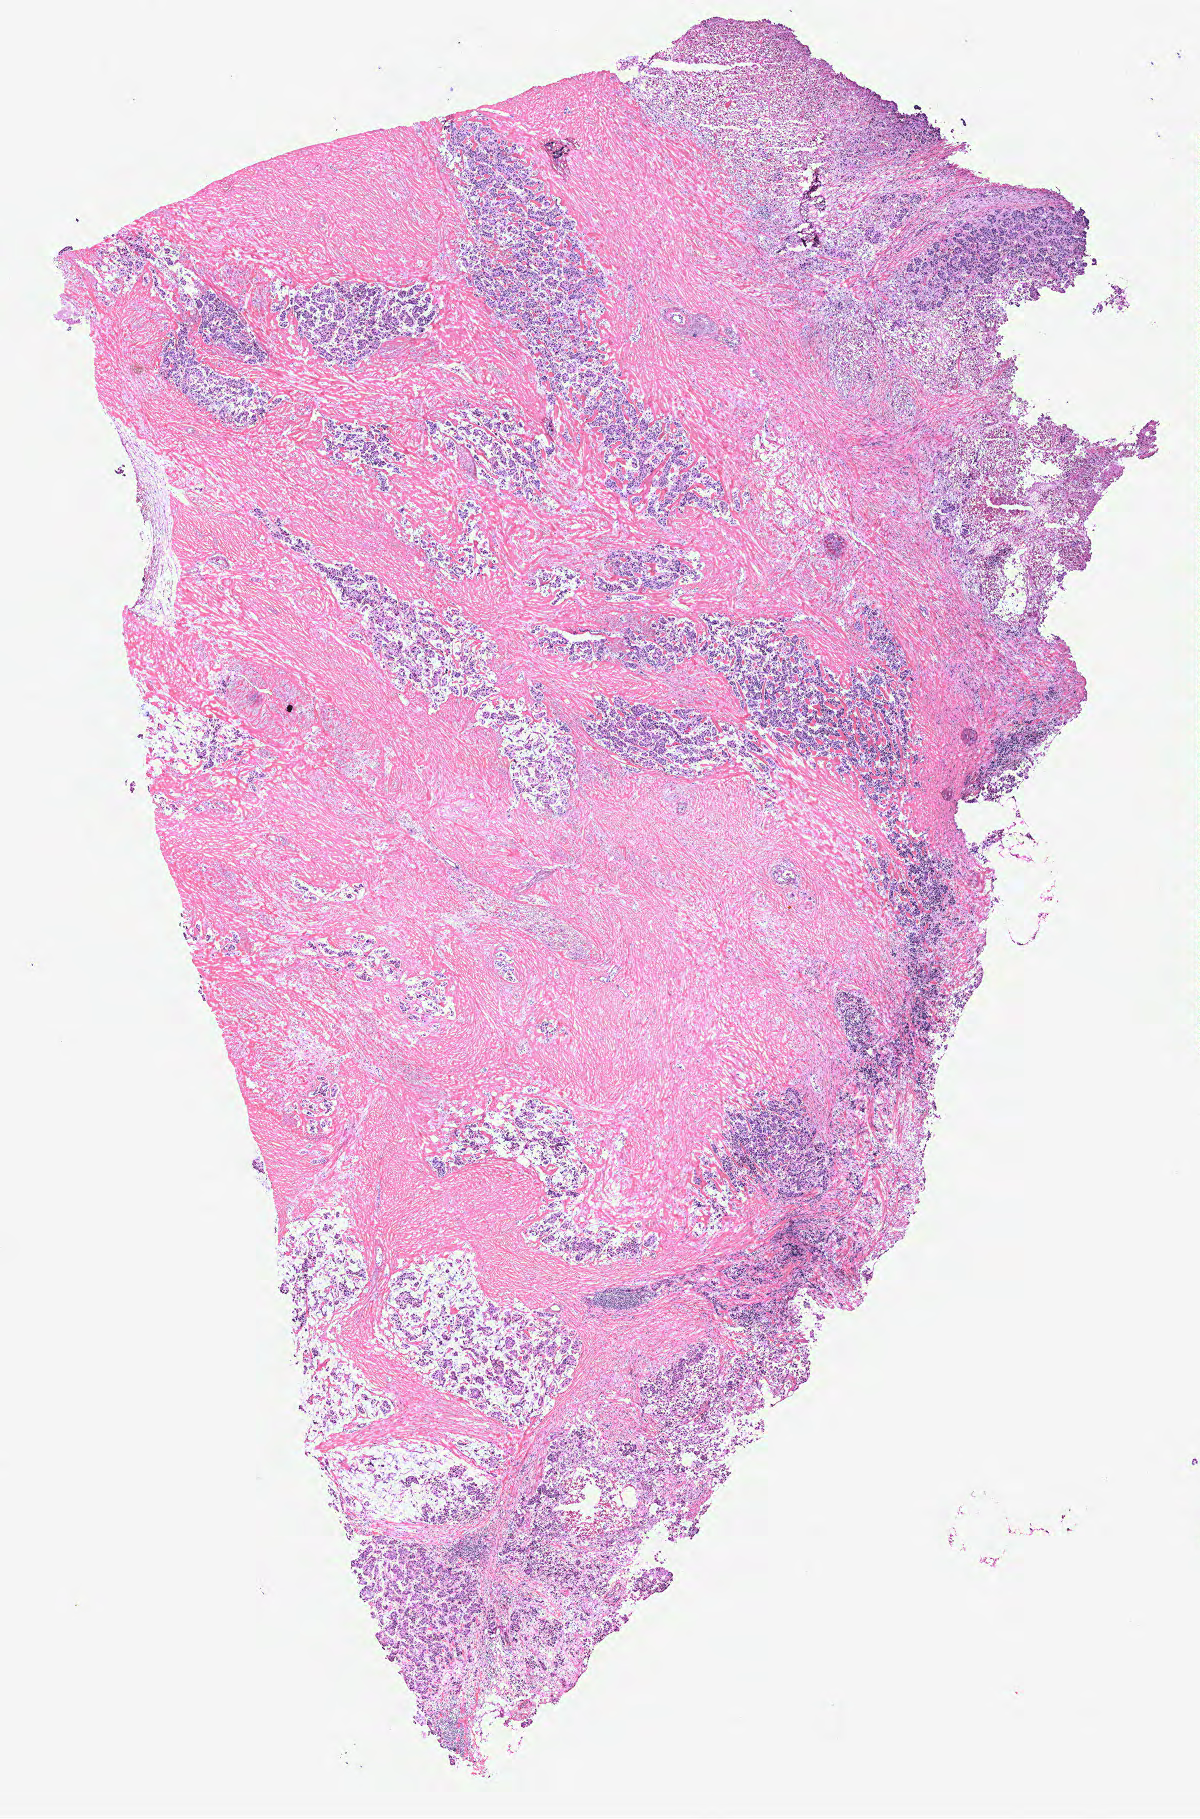
Digitized Hematoxylin and eosin (H&E) stained tissue section (whole slide), low-resolution overview of the scanned area, about 9.6 x 14.6 mm, breast, tissue type not recorded. Patient: female, age 72 years.
Patient diagnosis: Infiltrating duct carcinoma, NOS.